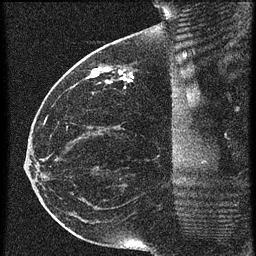
Breast MRI (dynamic contrast-enhanced), one sagittal slice. Position 26 of 60 along the scan axis. 3 images stored at this slice position (order not interpretable as contrast timing). 1.5 T. TE 4.2 ms, TR 20.4 ms. 256 × 256 image matrix, field of view 200 × 200 mm. Patient: female, 35 years. From the clinical record (not read from this slice): setting: breast cancer imaged before/during neoadjuvant chemotherapy; receptor status: HR-positive, HER2-negative.
Outlined on this slice (semi-automatically segmented with operator editing):
- analysis volume of interest (the breast-tissue region the enhancement analysis was run in; not a lesion): bounding box (x1, y1, x2, y2) in pixels: (84, 50, 179, 97)
- tumour enhancement mask (voxels above the 90 % enhancement threshold inside the analysis volume of interest): (90, 68, 127, 83)